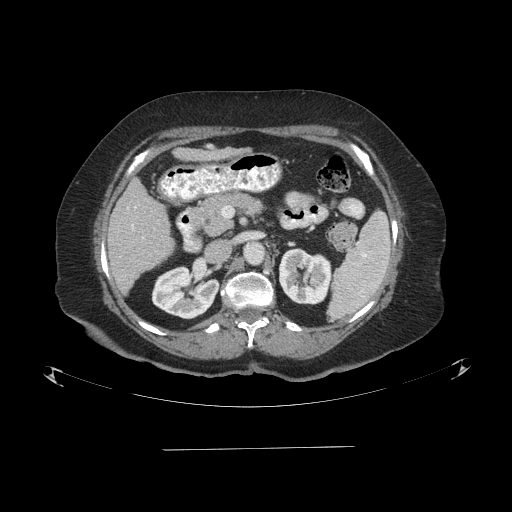
Contrast-enhanced abdominal CT (liver protocol), one axial slice. Position 39 of 103 along the scan axis. Reconstruction kernel STANDARD. 120 kVp. One of 2 acquisitions stored at this slice position. Soft-tissue window (W 400 / L 40 HU). 2.5 mm slice thickness. 512 × 512 image matrix, field of view 500 × 500 mm. From the clinical record (not read from this slice): diagnosis: hepatocellular carcinoma (patient treated with transarterial chemoembolisation; whether this scan precedes or follows treatment is not stated here); TNM stage (as recorded): Stage-IIIA; Child-Pugh class: A; tumour differentiation: poorly differentiated; tumour nodularity: multinodular.
Outlined on this slice (semi-automatically segmented with operator editing):
- liver parenchyma outside the tumour (the mass and vessels are separate outlines, so this box may not span the whole liver): bounding box (x1, y1, x2, y2) in pixels: (108, 178, 174, 292)